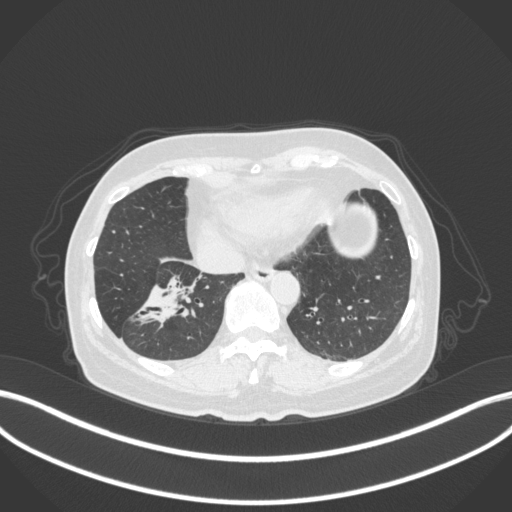
Chest CT, one axial slice. Position 113 of 429 along the scan axis. Reconstruction kernel B31f. 120 kVp. Lung window (W 1500 / L -600 HU). 512 × 512 image matrix. Patient: female, 67 years. Case-level facts recorded for this patient, not image findings: clinical TNM (as recorded): T1c N1 M0; histopathological grade: G2-3.
Structures marked on this image (bounding box drawn by a radiologist):
- lung tumour (recorded histology: adenocarcinoma): bounding box <126,271,201,330> (left, top, right, bottom; pixels)